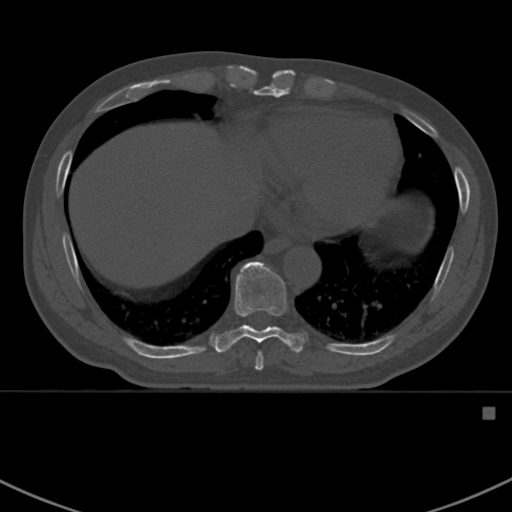
CT including the spine, one axial slice; slice 383 of 412 in the series (ordered by position); reconstruction kernel Br40s; 120 kVp; bone window (W 1800 / L 400 HU); 1.5 mm slice thickness; 512 × 512 image matrix, field of view 358 × 358 mm. Male patient, age 59 years. From the clinical record (not read from this slice): primary cancer: prostate.
Annotated regions visible in this slice (semi-automatically segmented with operator editing):
- T8 vertebra: box from (x=255, y=353) to (x=263, y=371) px
- T9 vertebra: (x=211, y=261)–(x=304, y=353)